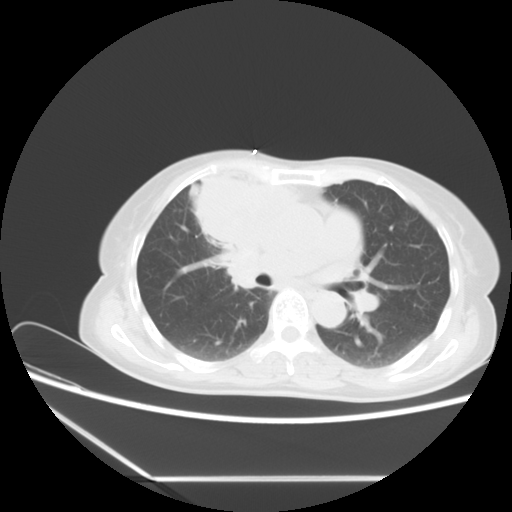
Chest CT, one axial slice; slice 9 of 16 in the series (ordered by position); lung window (W 1500 / L -600 HU); 5 mm slice thickness; 512 × 512 image matrix, field of view 350 × 350 mm. Patient: female, 63 years. Case-level facts recorded for this patient, not image findings: clinical TNM (as recorded): T2b N1 M0.
Outlined on this slice (rectangle marked by the reading radiologist):
- lung tumour (recorded histology: adenocarcinoma): box from (x=194, y=161) to (x=305, y=250) px